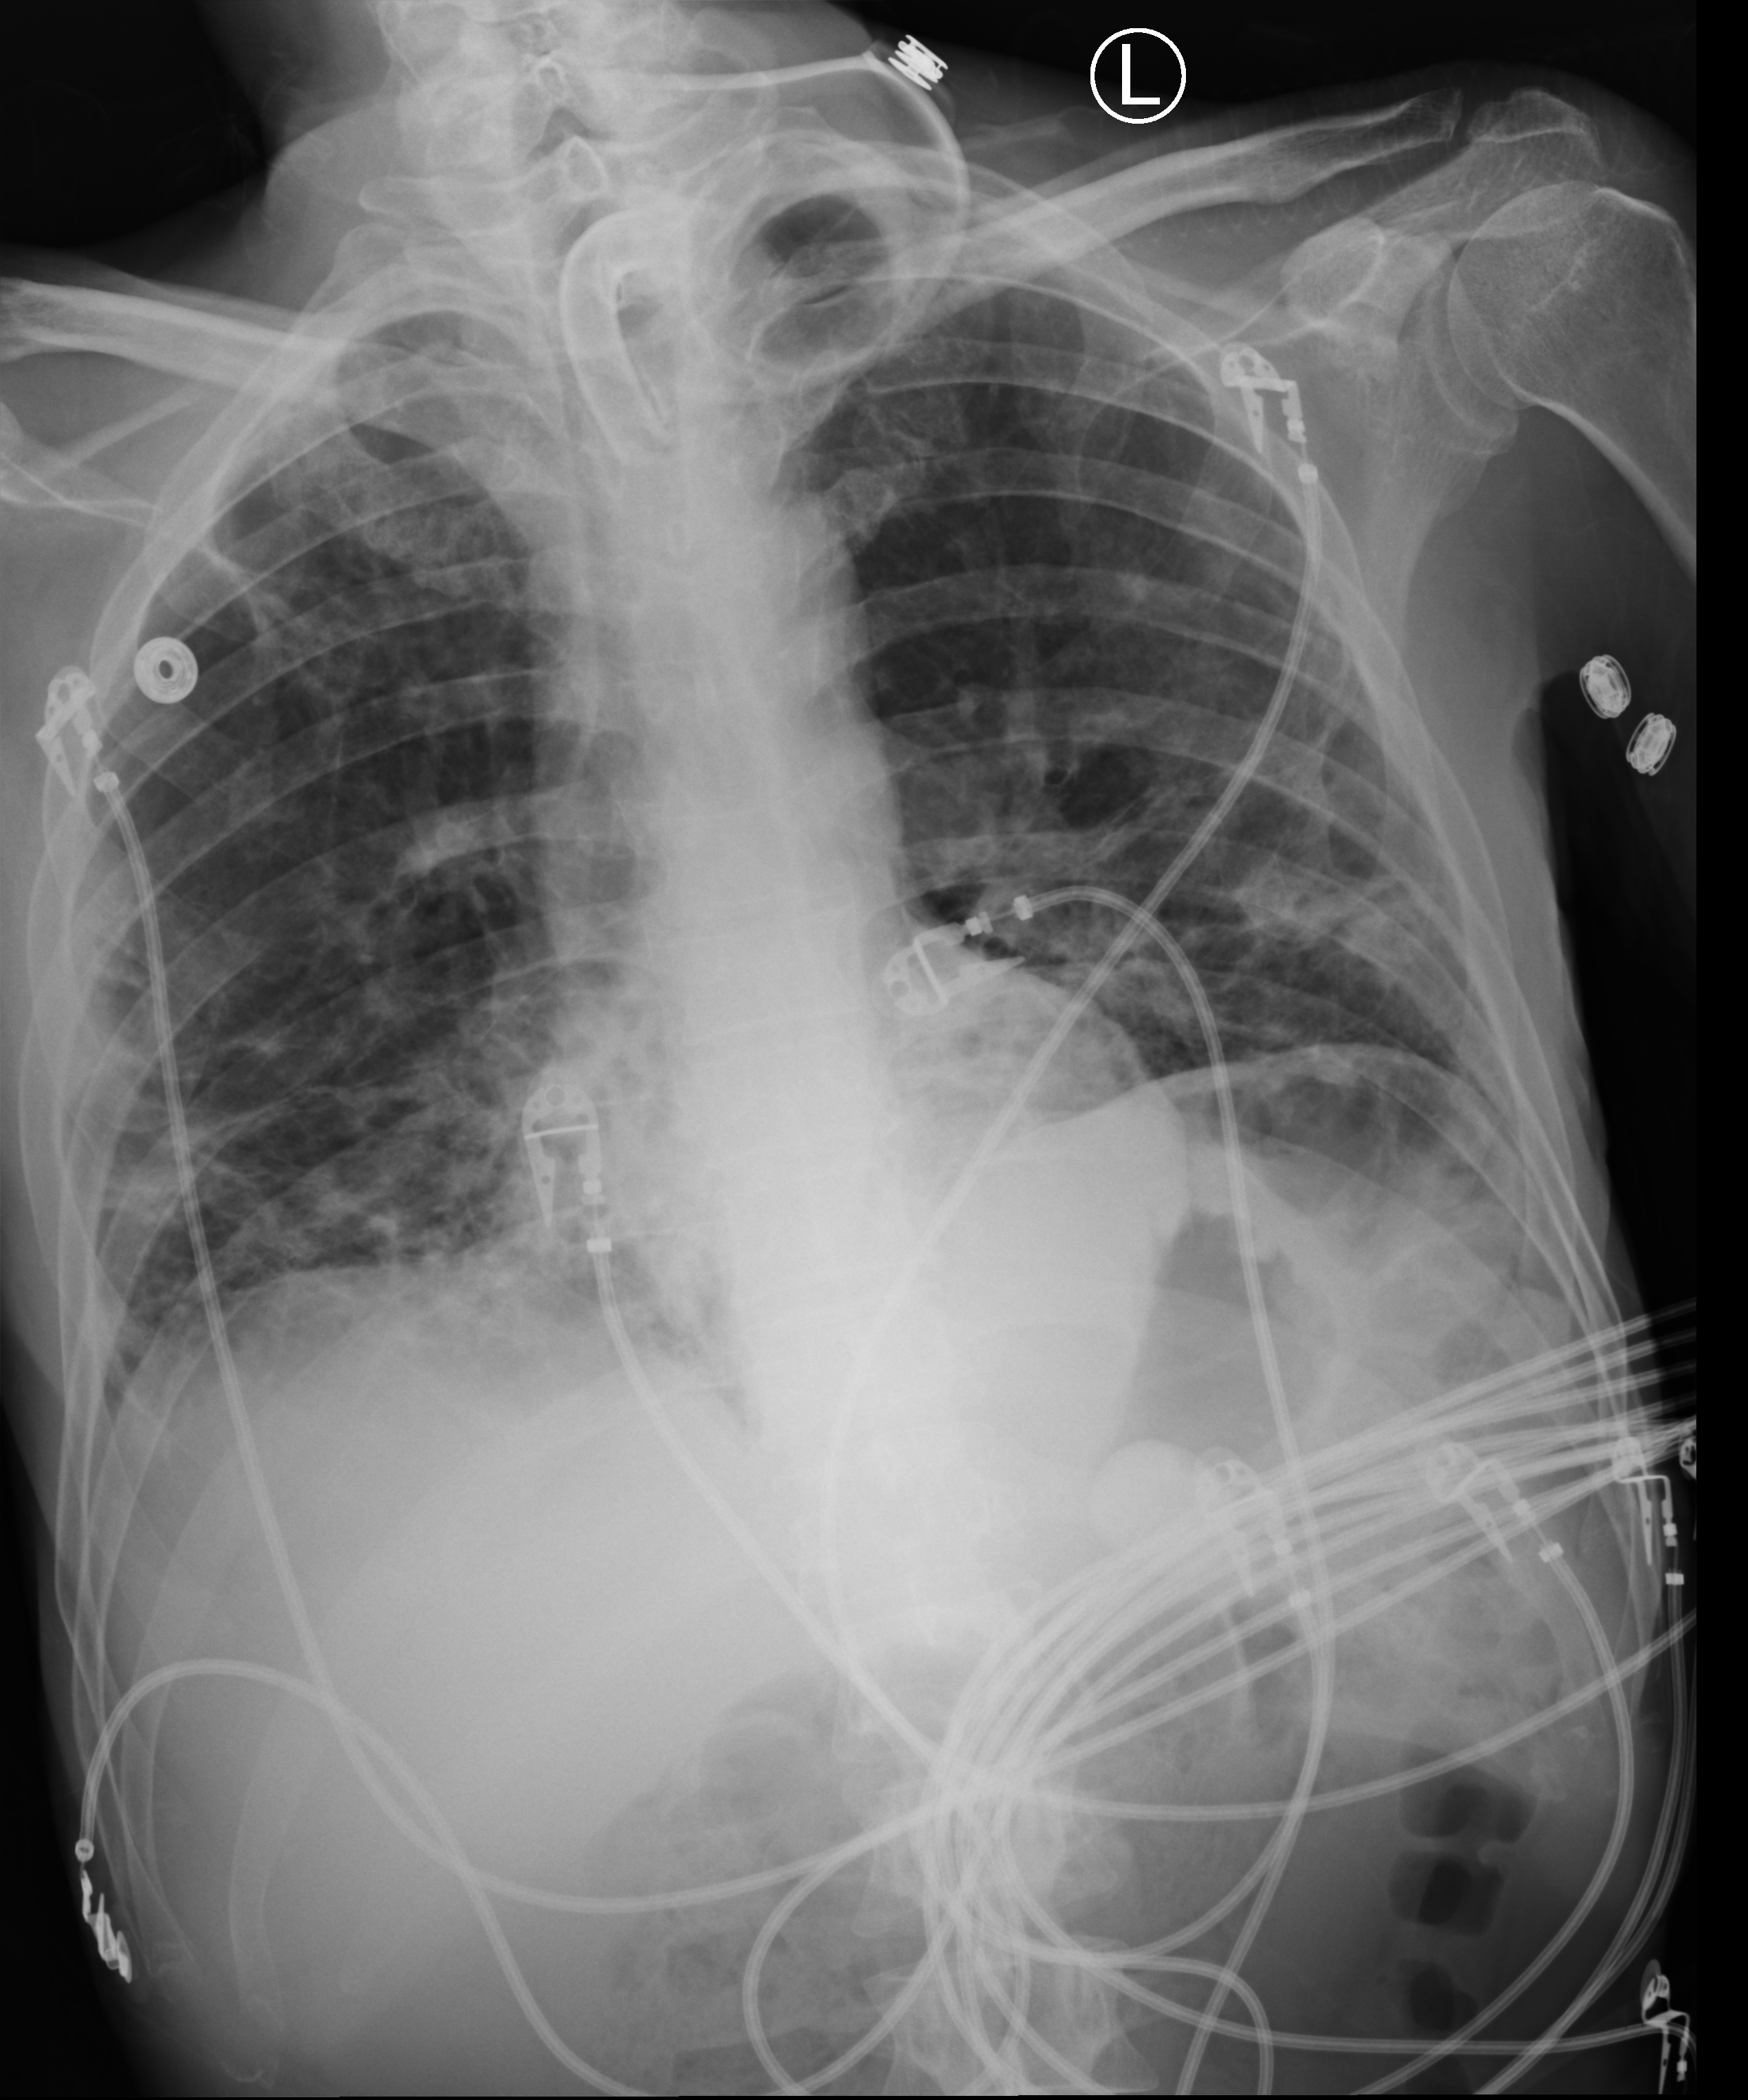
Bedside chest radiograph (computed radiography); anteroposterior (AP) projection. Male patient hospitalised with COVID-19, age 18–59 years.
From the hospital-stay record, not from the radiograph (when in the stay this image was taken is not recorded): mechanically ventilated during this hospital stay: yes; admitted to intensive care during this hospital stay: yes; hypertension (admission record): yes.